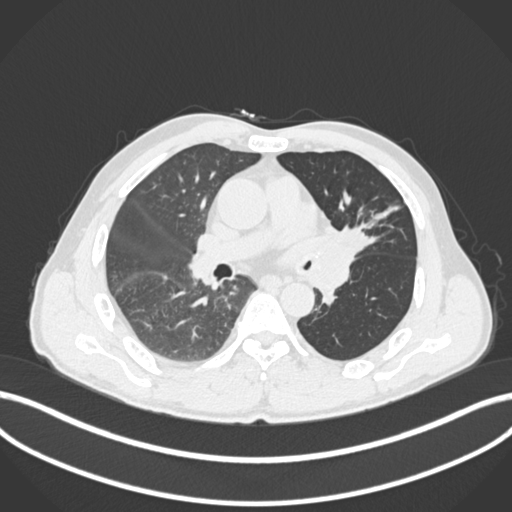
Chest CT, one axial slice; slice 102 of 255 in the series (ordered by position); 120 kVp; lung window (W 1500 / L -600 HU); 1 mm slice thickness; 512 × 512 image matrix, field of view 400 × 400 mm. Patient: male, 57 years. Case-level facts recorded for this patient, not image findings: clinical TNM (as recorded): T2b N0 M0.
Structures marked on this image (rectangle marked by the reading radiologist):
- lung tumour (recorded histology: squamous cell carcinoma): bounding box [x1, y1, x2, y2] px = [312, 219, 375, 264]